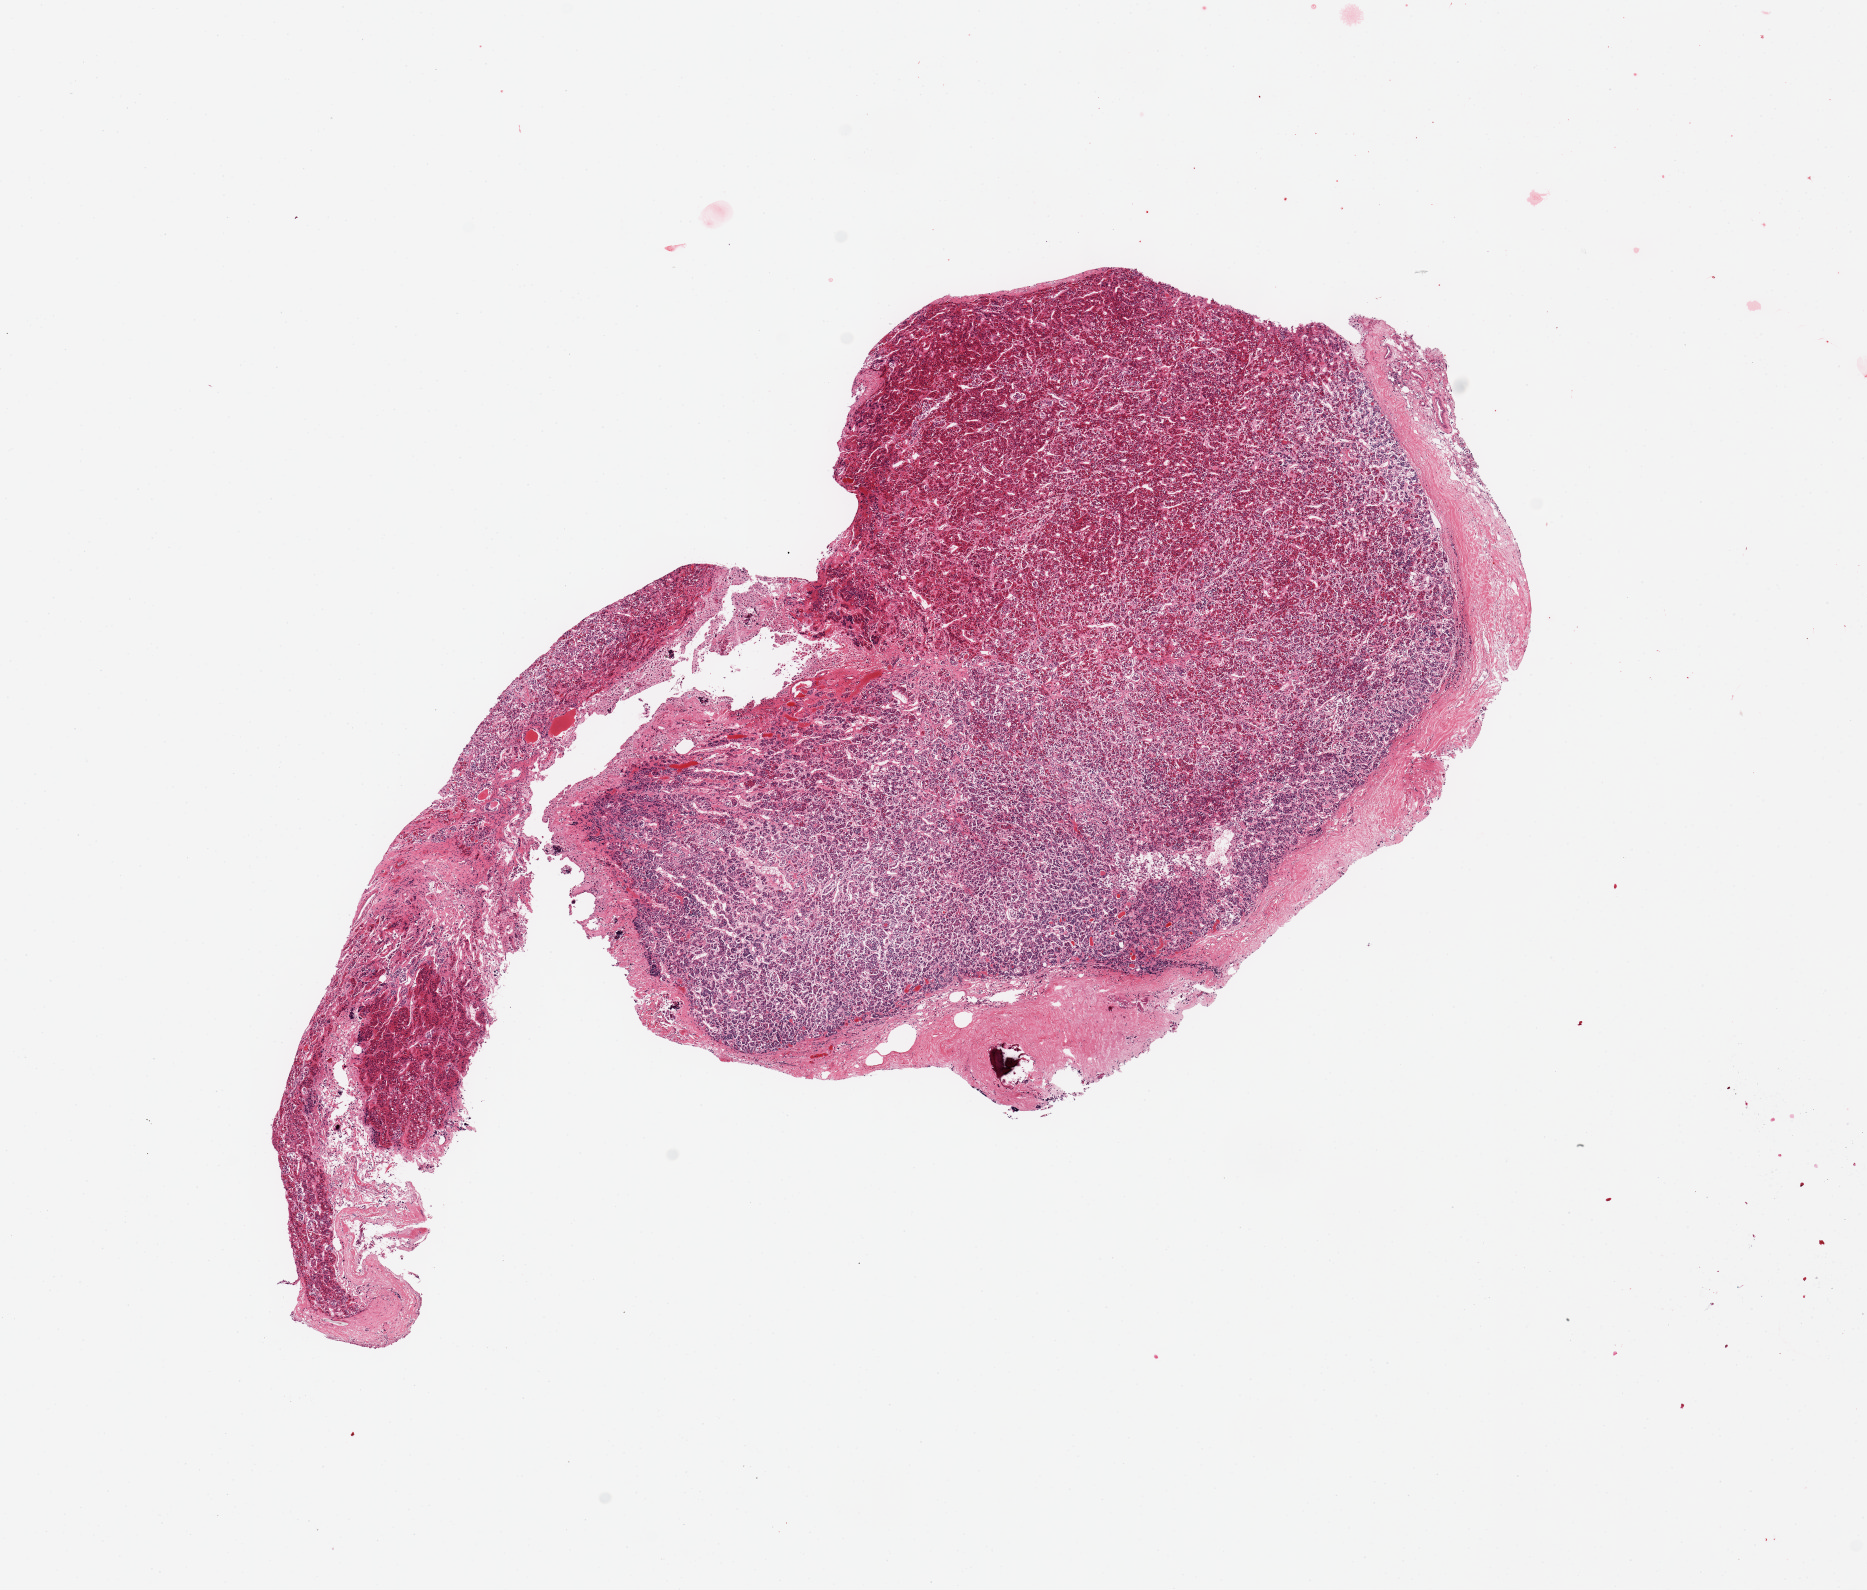
Digitized H&E-stained section, brightfield, a low-resolution overview of the entire scanned area, about 14.8 x 12.6 mm (acquisition: 20x scan), PAXgene-fixed paraffin-embedded (PFPE) section, sampled site (target tissue): pituitary, donor tissue sample. Male donor.
- pathologist's review note for this sample: 1 piece, adenohypophysis, partial rim of dura up to ~0.4mm